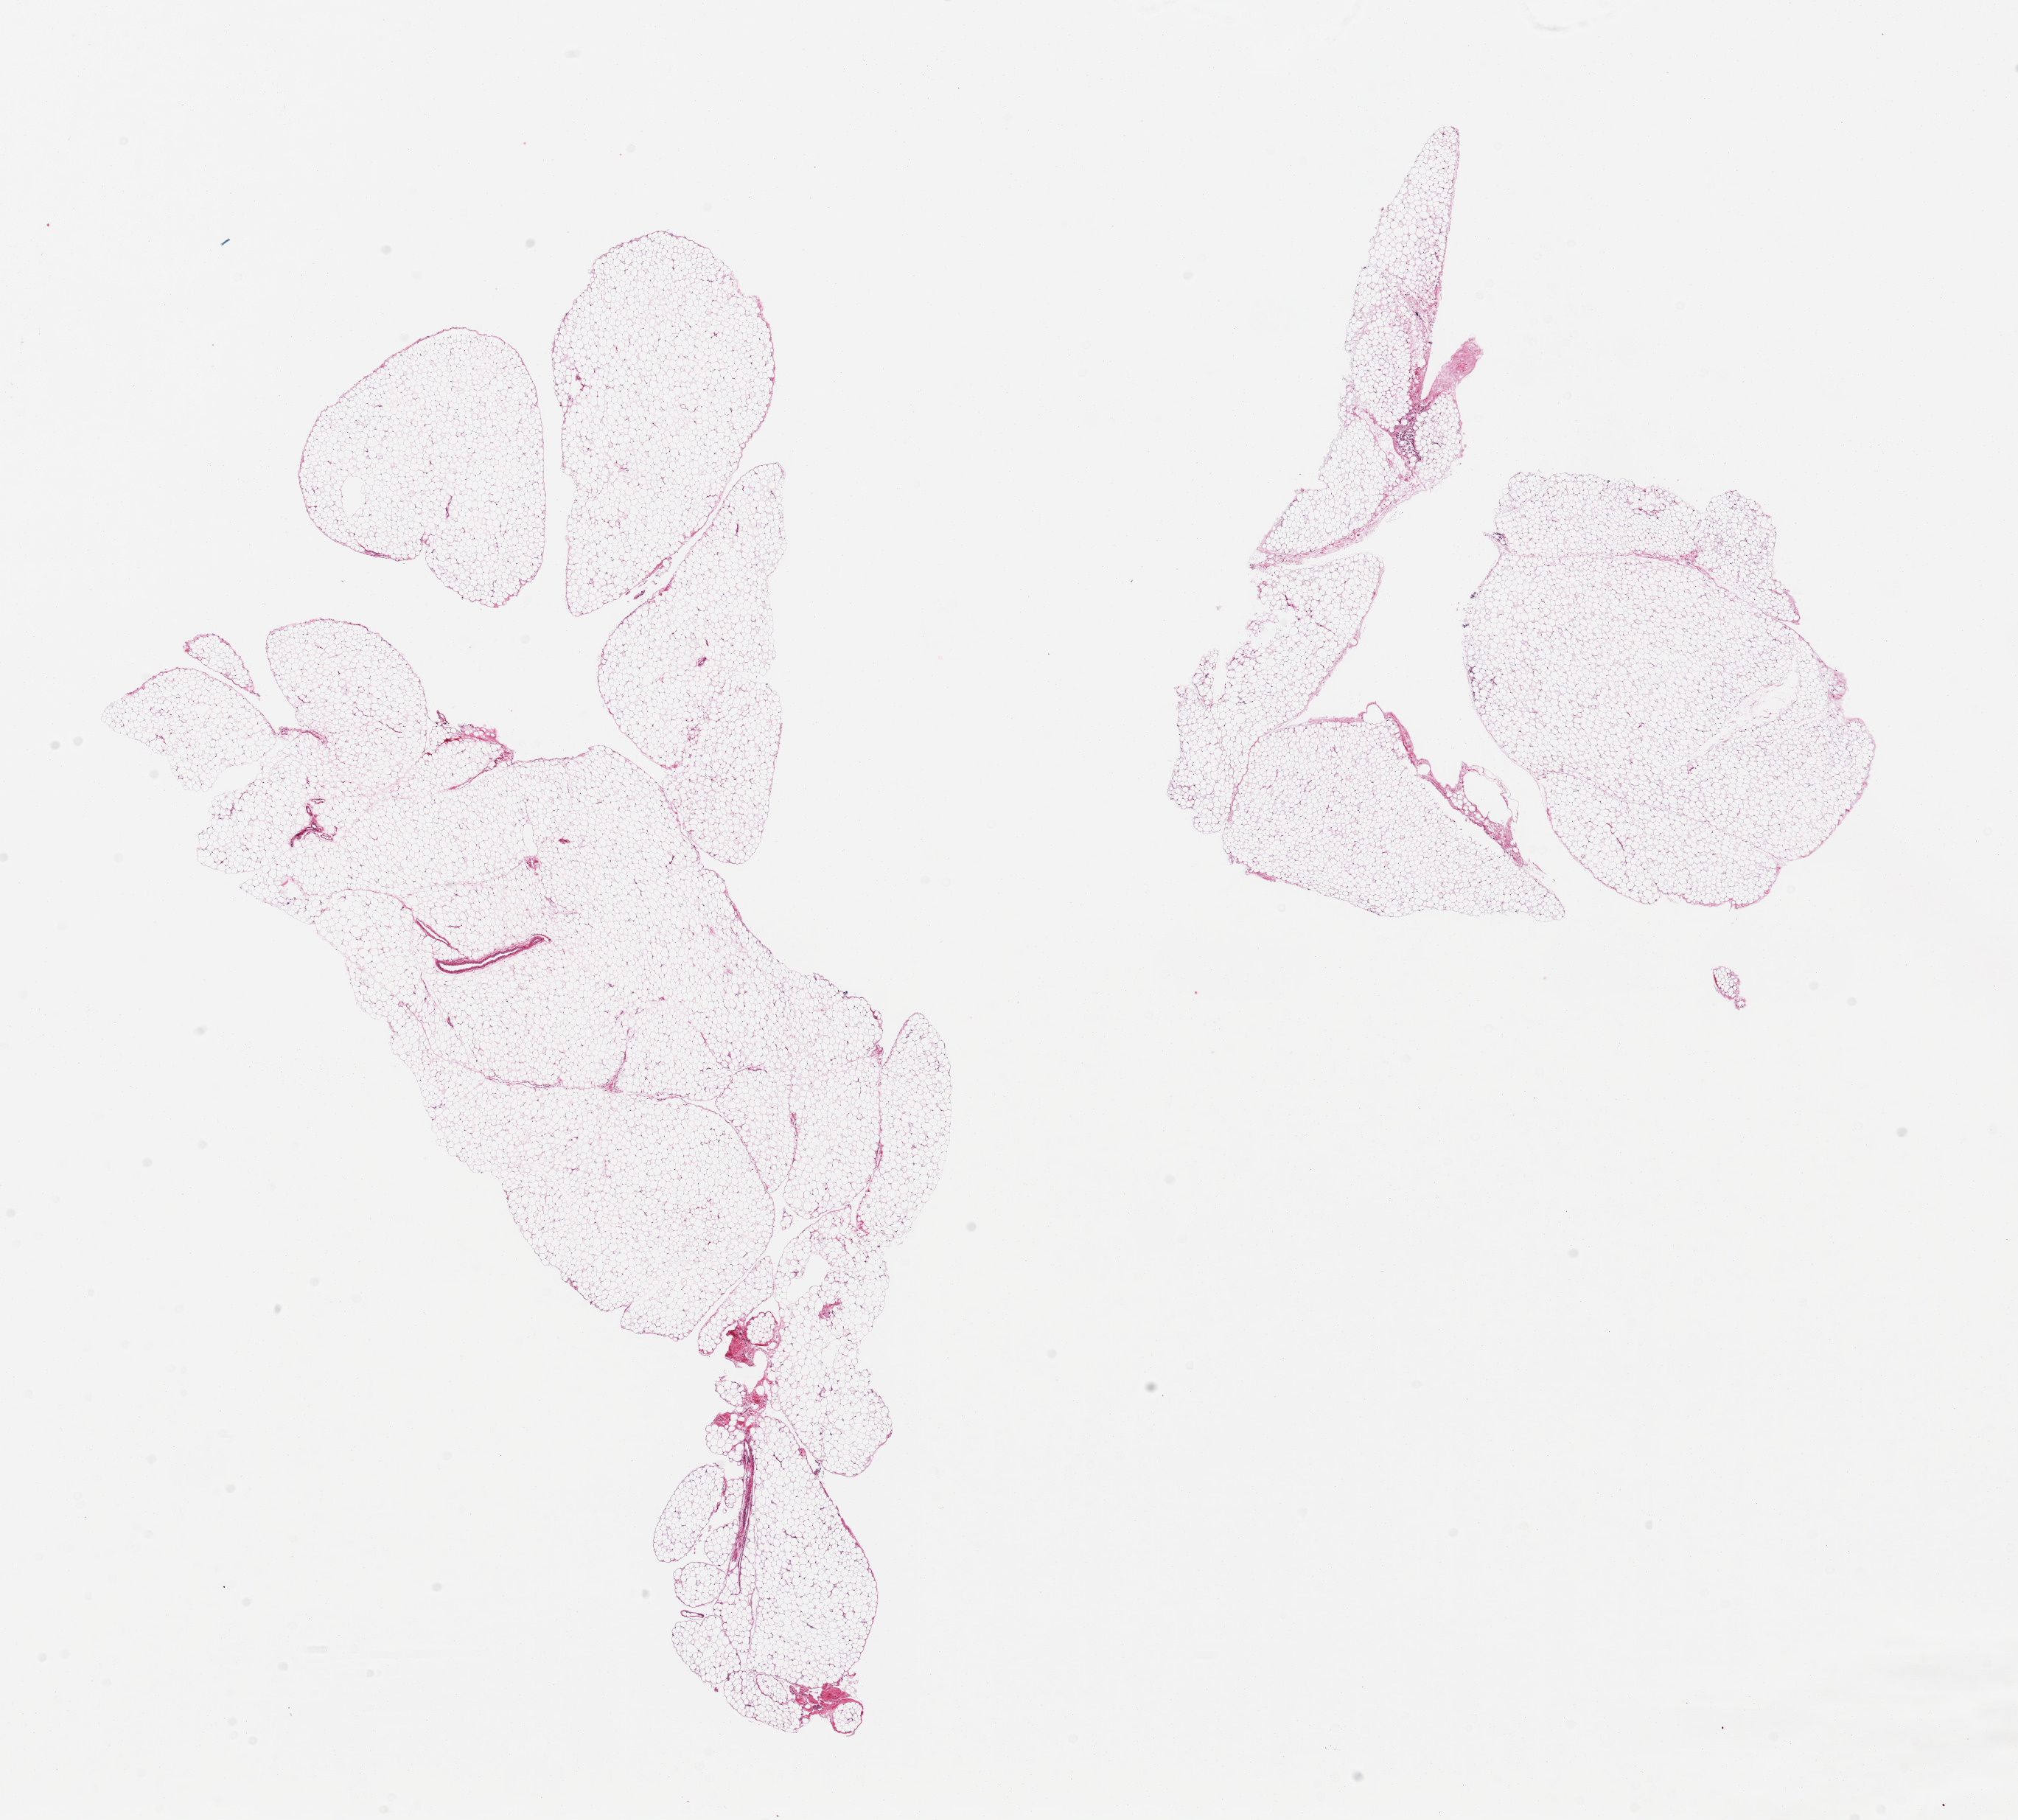
H&E whole-slide image, brightfield — shown as a low-resolution overview of the whole scanned area (about 21.7 x 19.5 mm, from a 20x scan). PAXgene-fixed paraffin-embedded (PFPE) section. Target tissue: omentum. Donor tissue sample. Donor: male.
• reviewer comment on this tissue sample: 2 pieces, trace mesothelium/fascia